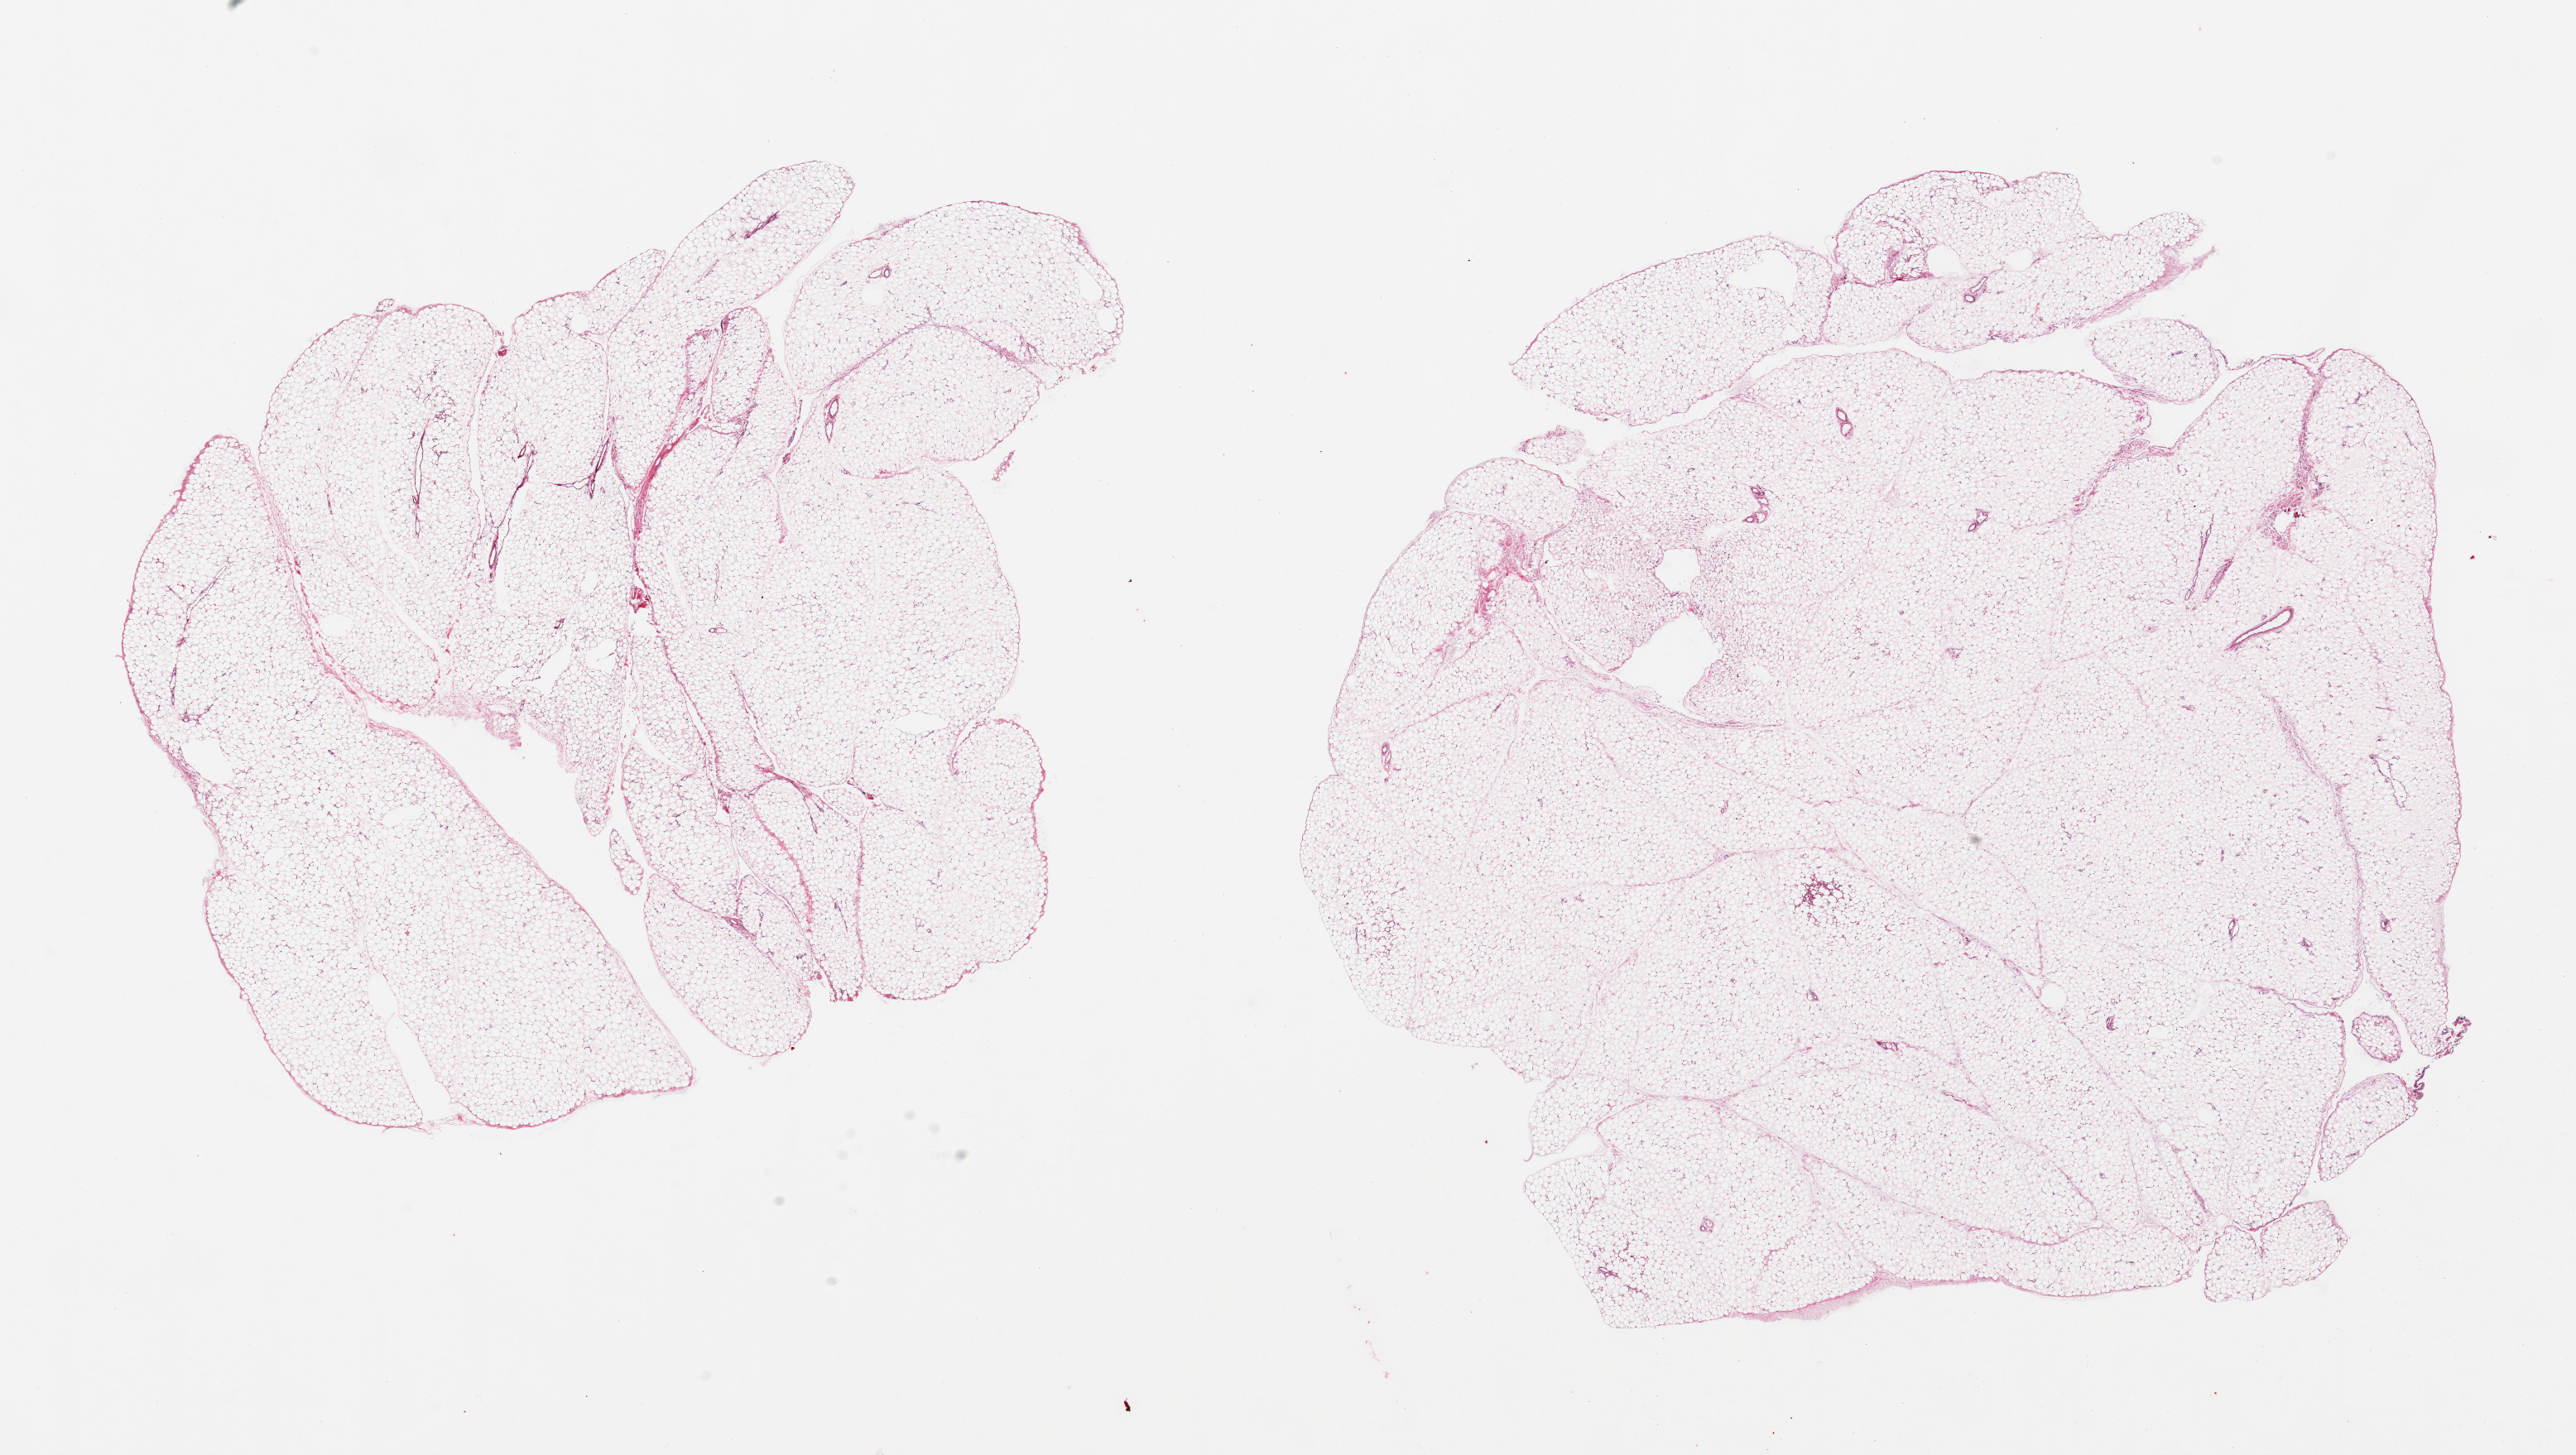
H&E whole-slide image — a low-resolution overview of the entire scanned area, about 24.6 x 13.9 mm (slide scanned at 20x); PAXgene-fixed, paraffin-embedded tissue; section of omentum (target tissue); donor tissue sample.
* pathologist's review note for this sample: 2 pieces; adipose tissue with minimal fibrous content